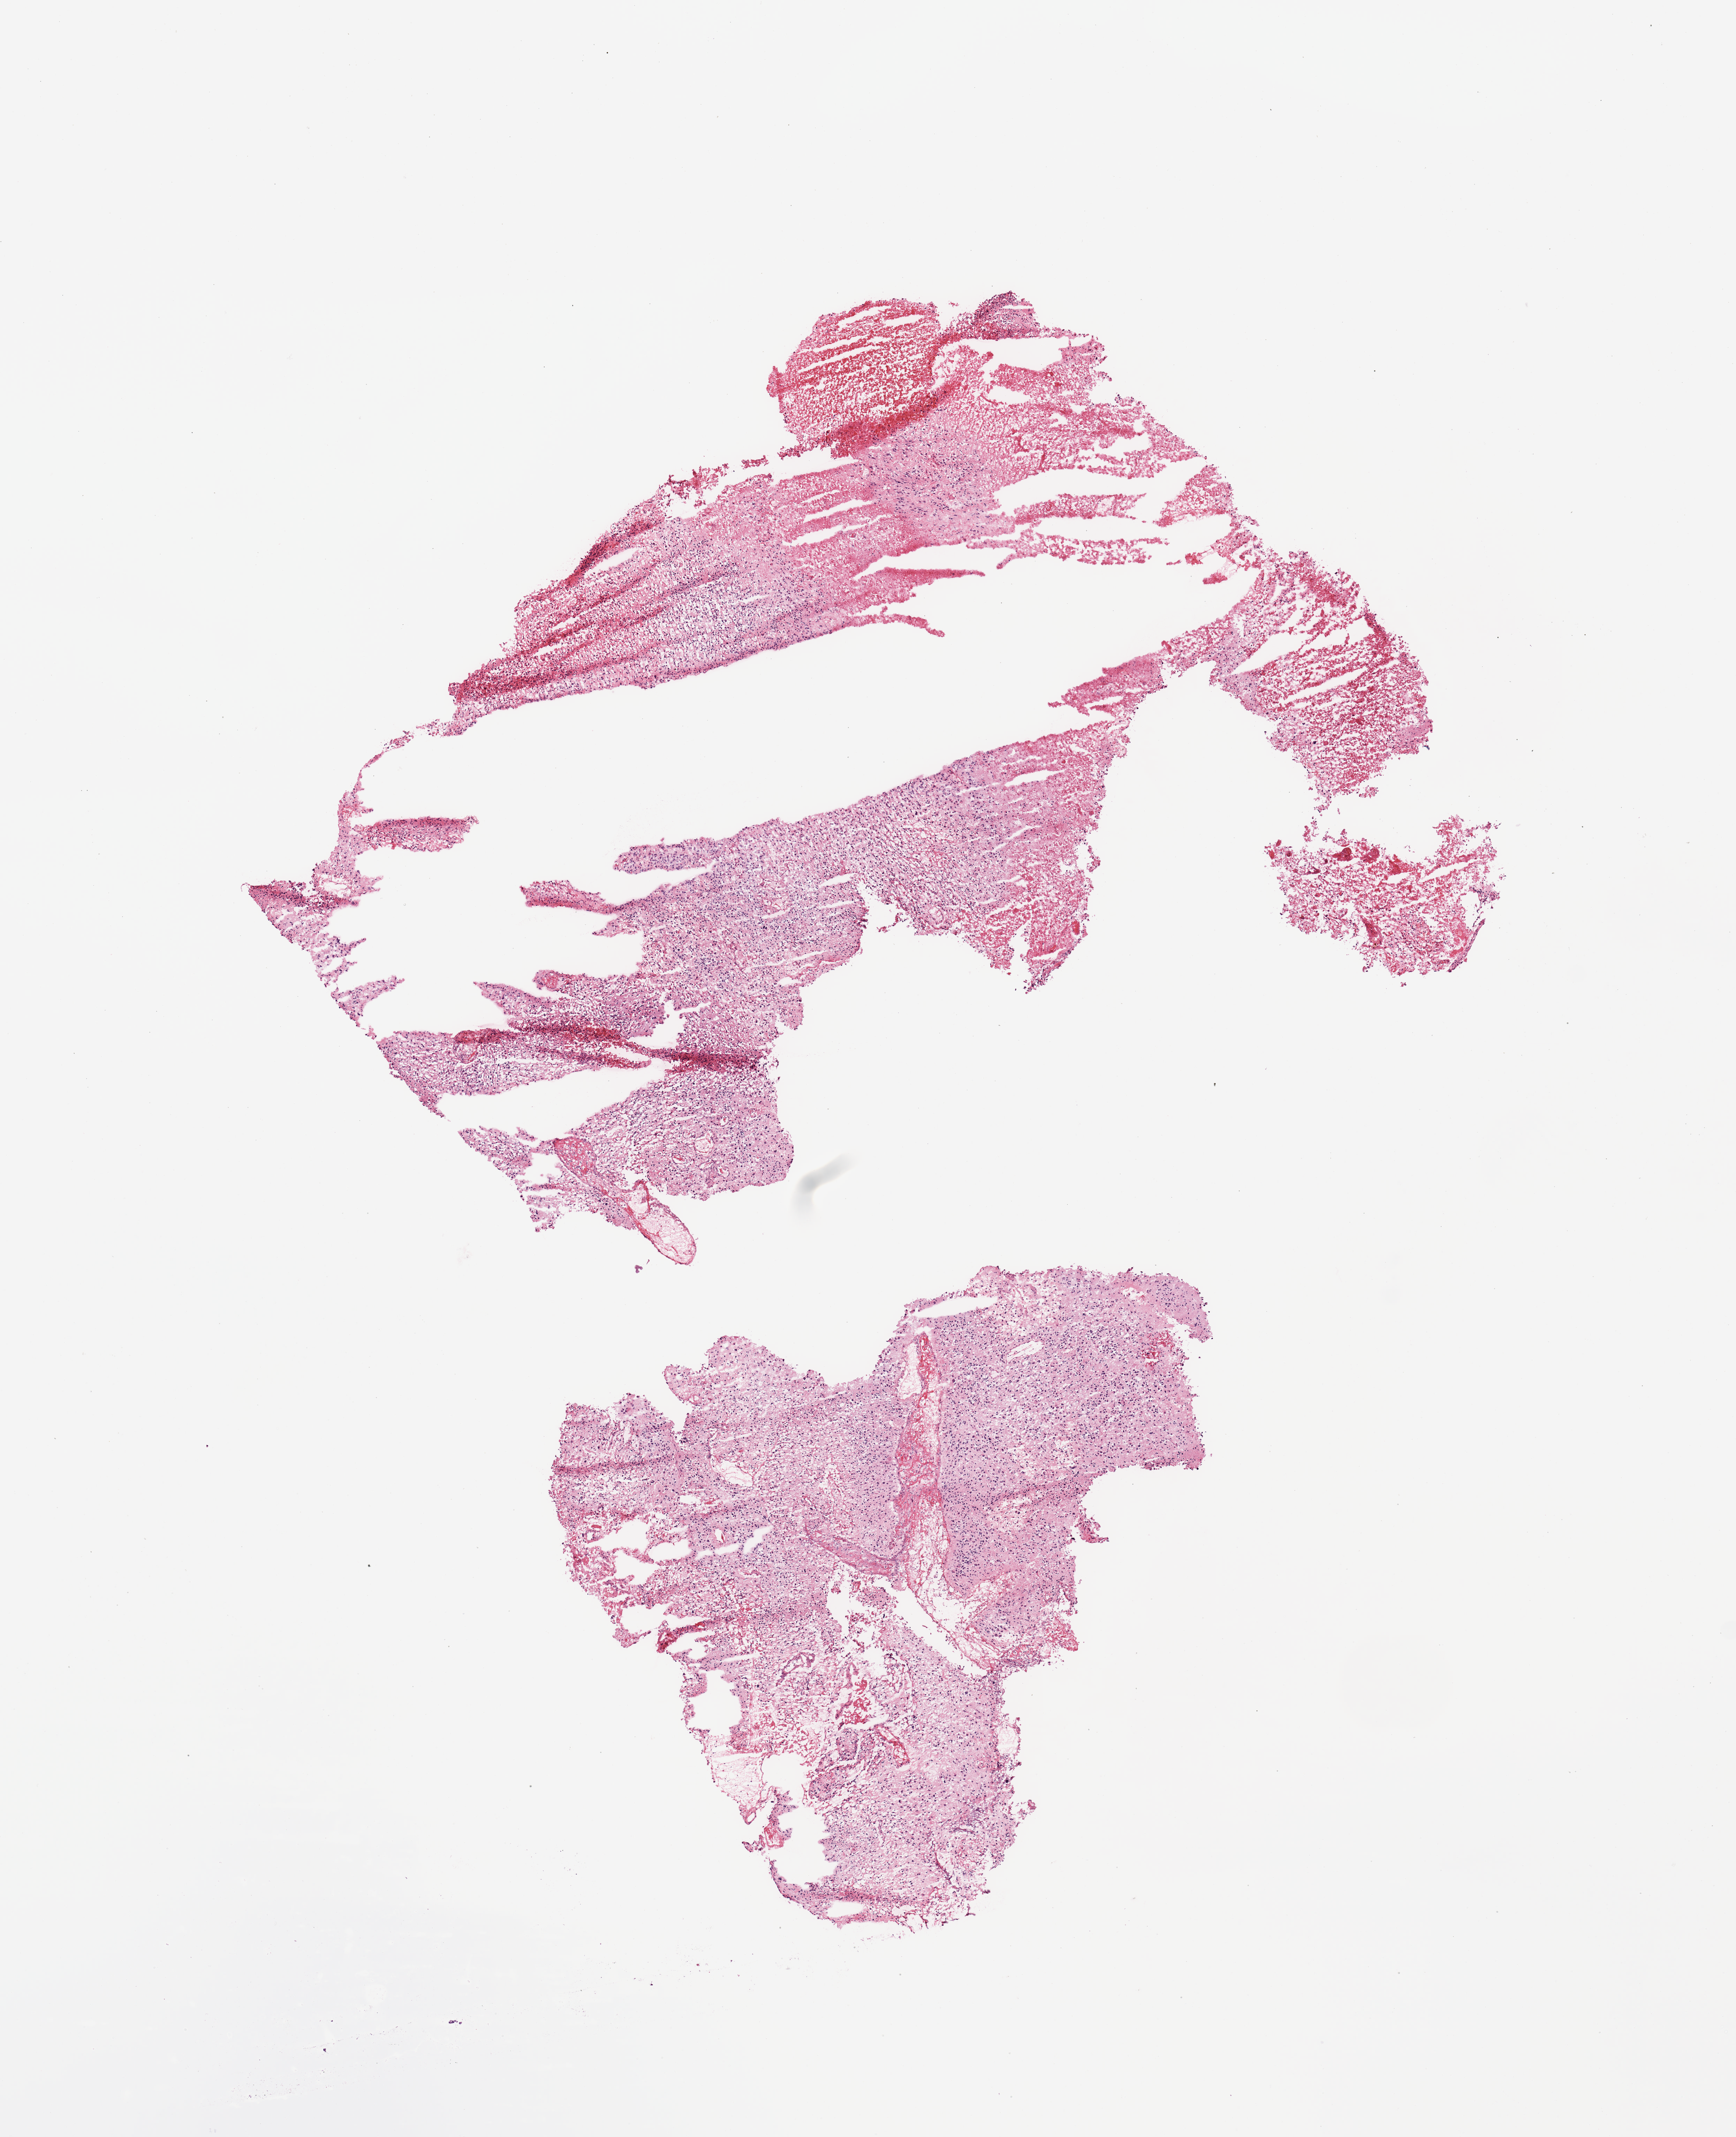
Hematoxylin and eosin (H&E) stained whole-slide image, low-resolution overview of the scanned area, about 9.8 x 12.1 mm (from a 20x scan); brain, tissue type not recorded.
Patient diagnosis (cohort enrolment): glioblastoma multiforme (brain).